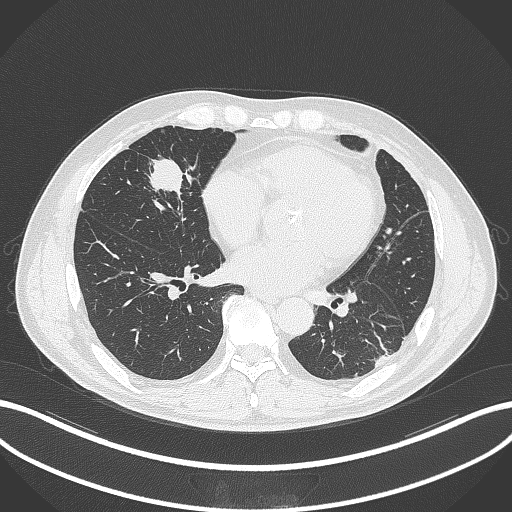
Chest CT, one axial slice. Slice 114 of 399 in the series (ordered by position). 120 kVp. Lung window (W 1500 / L -600 HU). 512 × 512 image matrix, field of view 400 × 400 mm. Male patient, age 59 years. Case-level facts recorded for this patient, not image findings: clinical TNM (as recorded): T2a N1 M0.
Outlined on this slice (bounding box drawn by a radiologist):
- lung tumour (recorded histology: adenocarcinoma): bounding box [x1, y1, x2, y2] px = [140, 150, 194, 203]